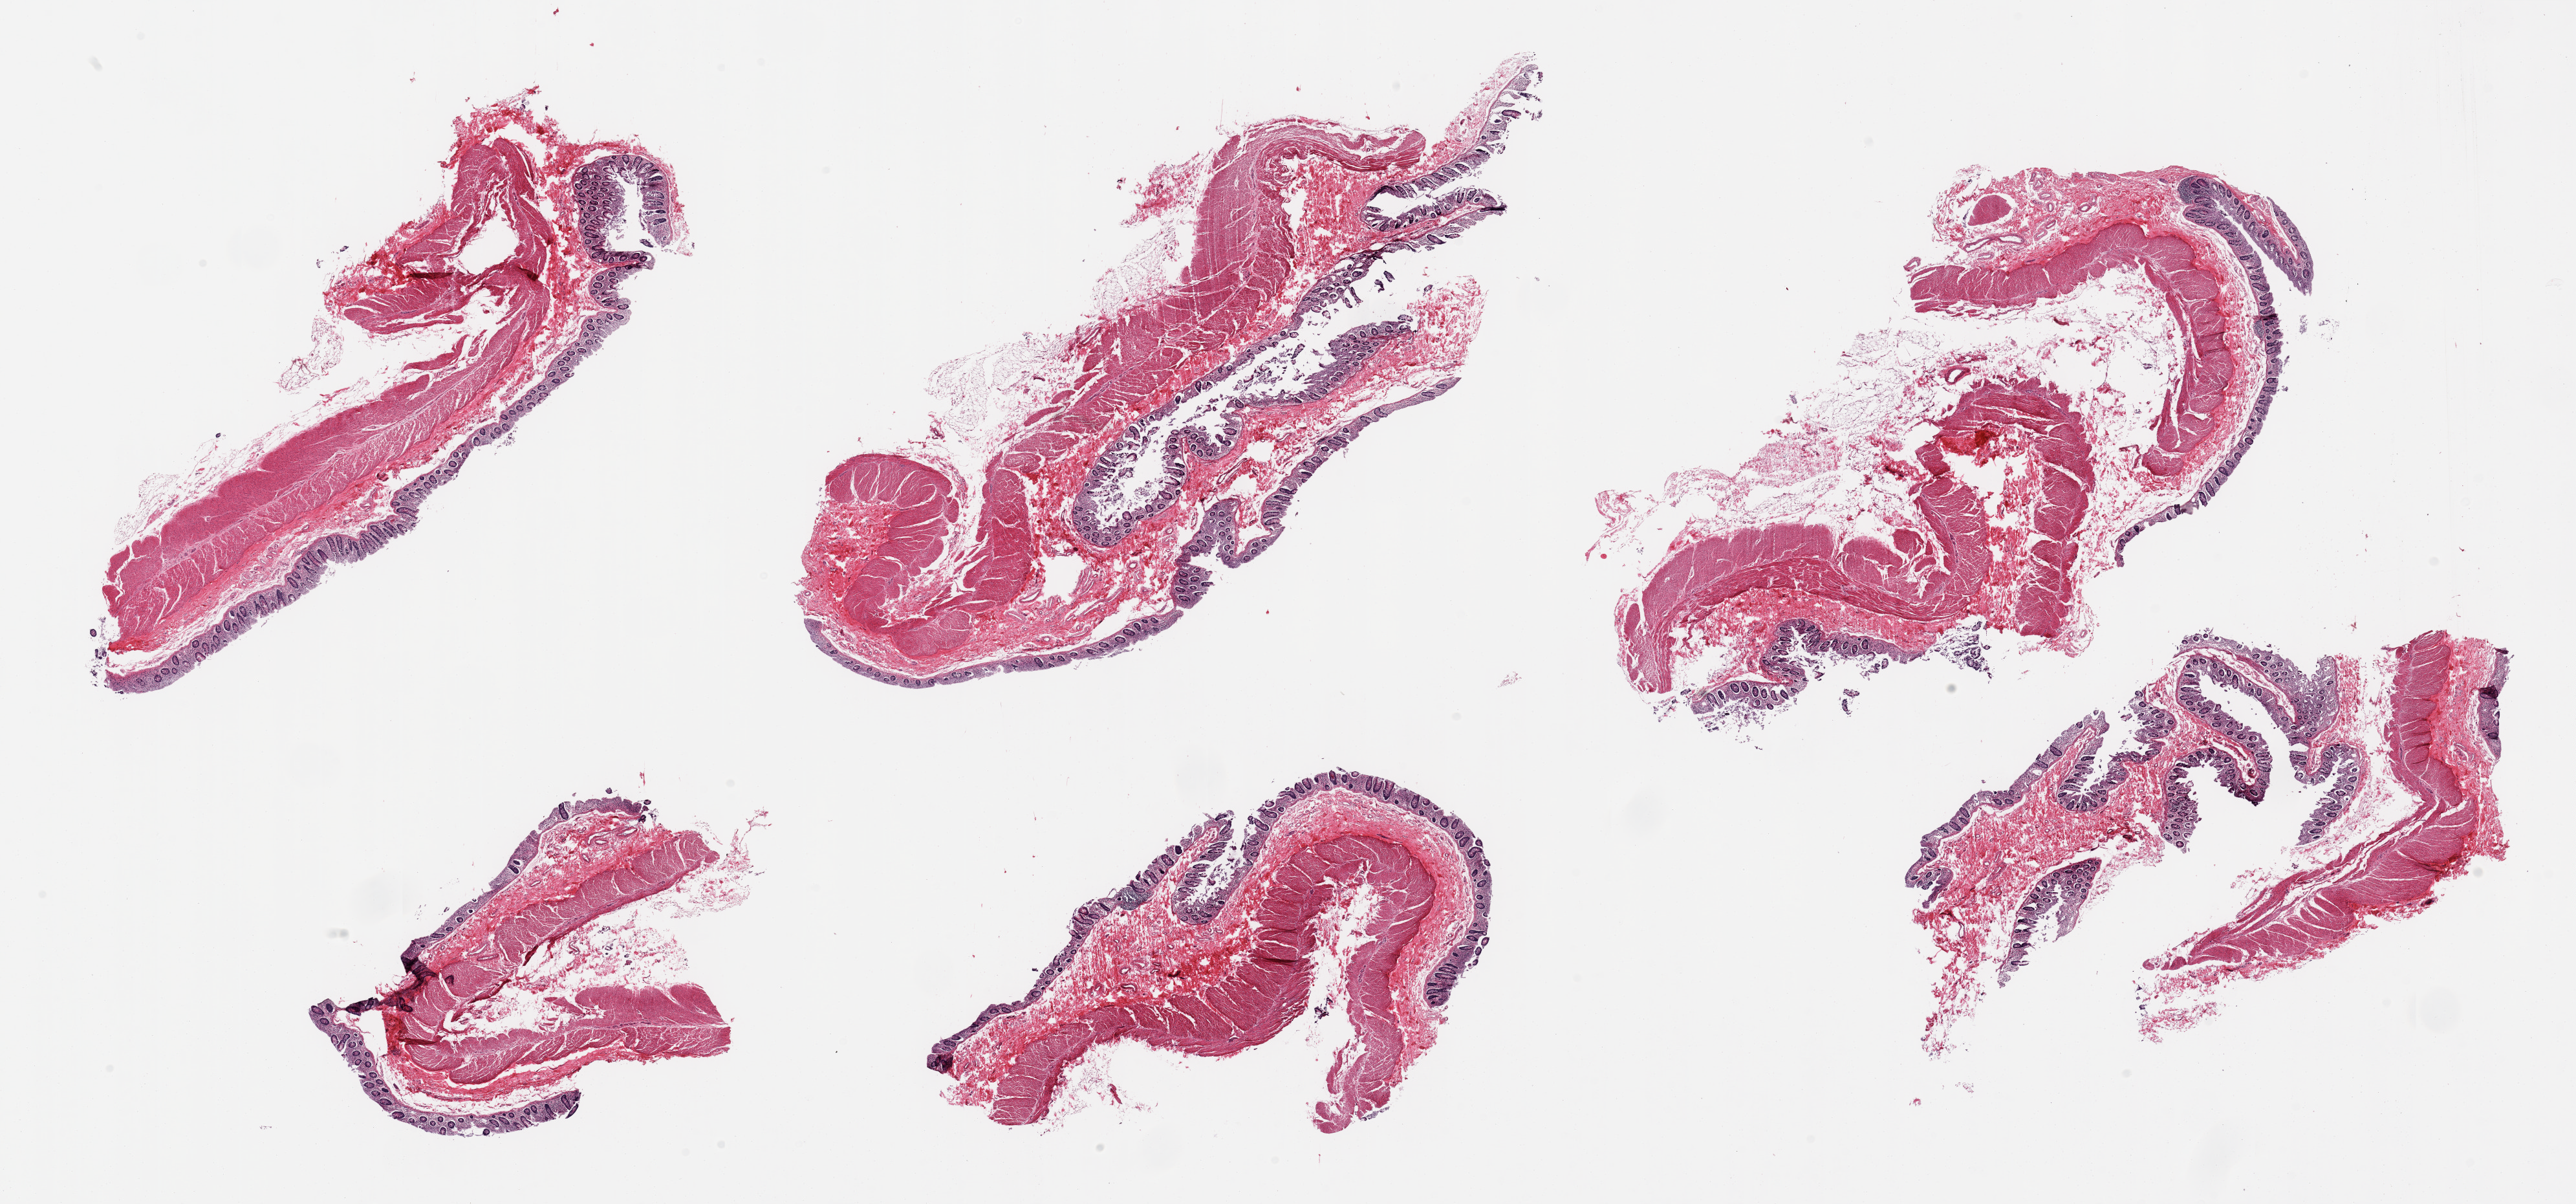
H&E whole-slide image, low-resolution overview of the scanned area, about 31.5 x 14.7 mm (slide scanned at 20x); PAXgene-fixed, paraffin-embedded tissue; target tissue: transverse colon; tissue donor sample. Donor: female.
* pathologist's review note for this sample: 6 pieces; full thickness sections, moderate autolysis, some attached fat